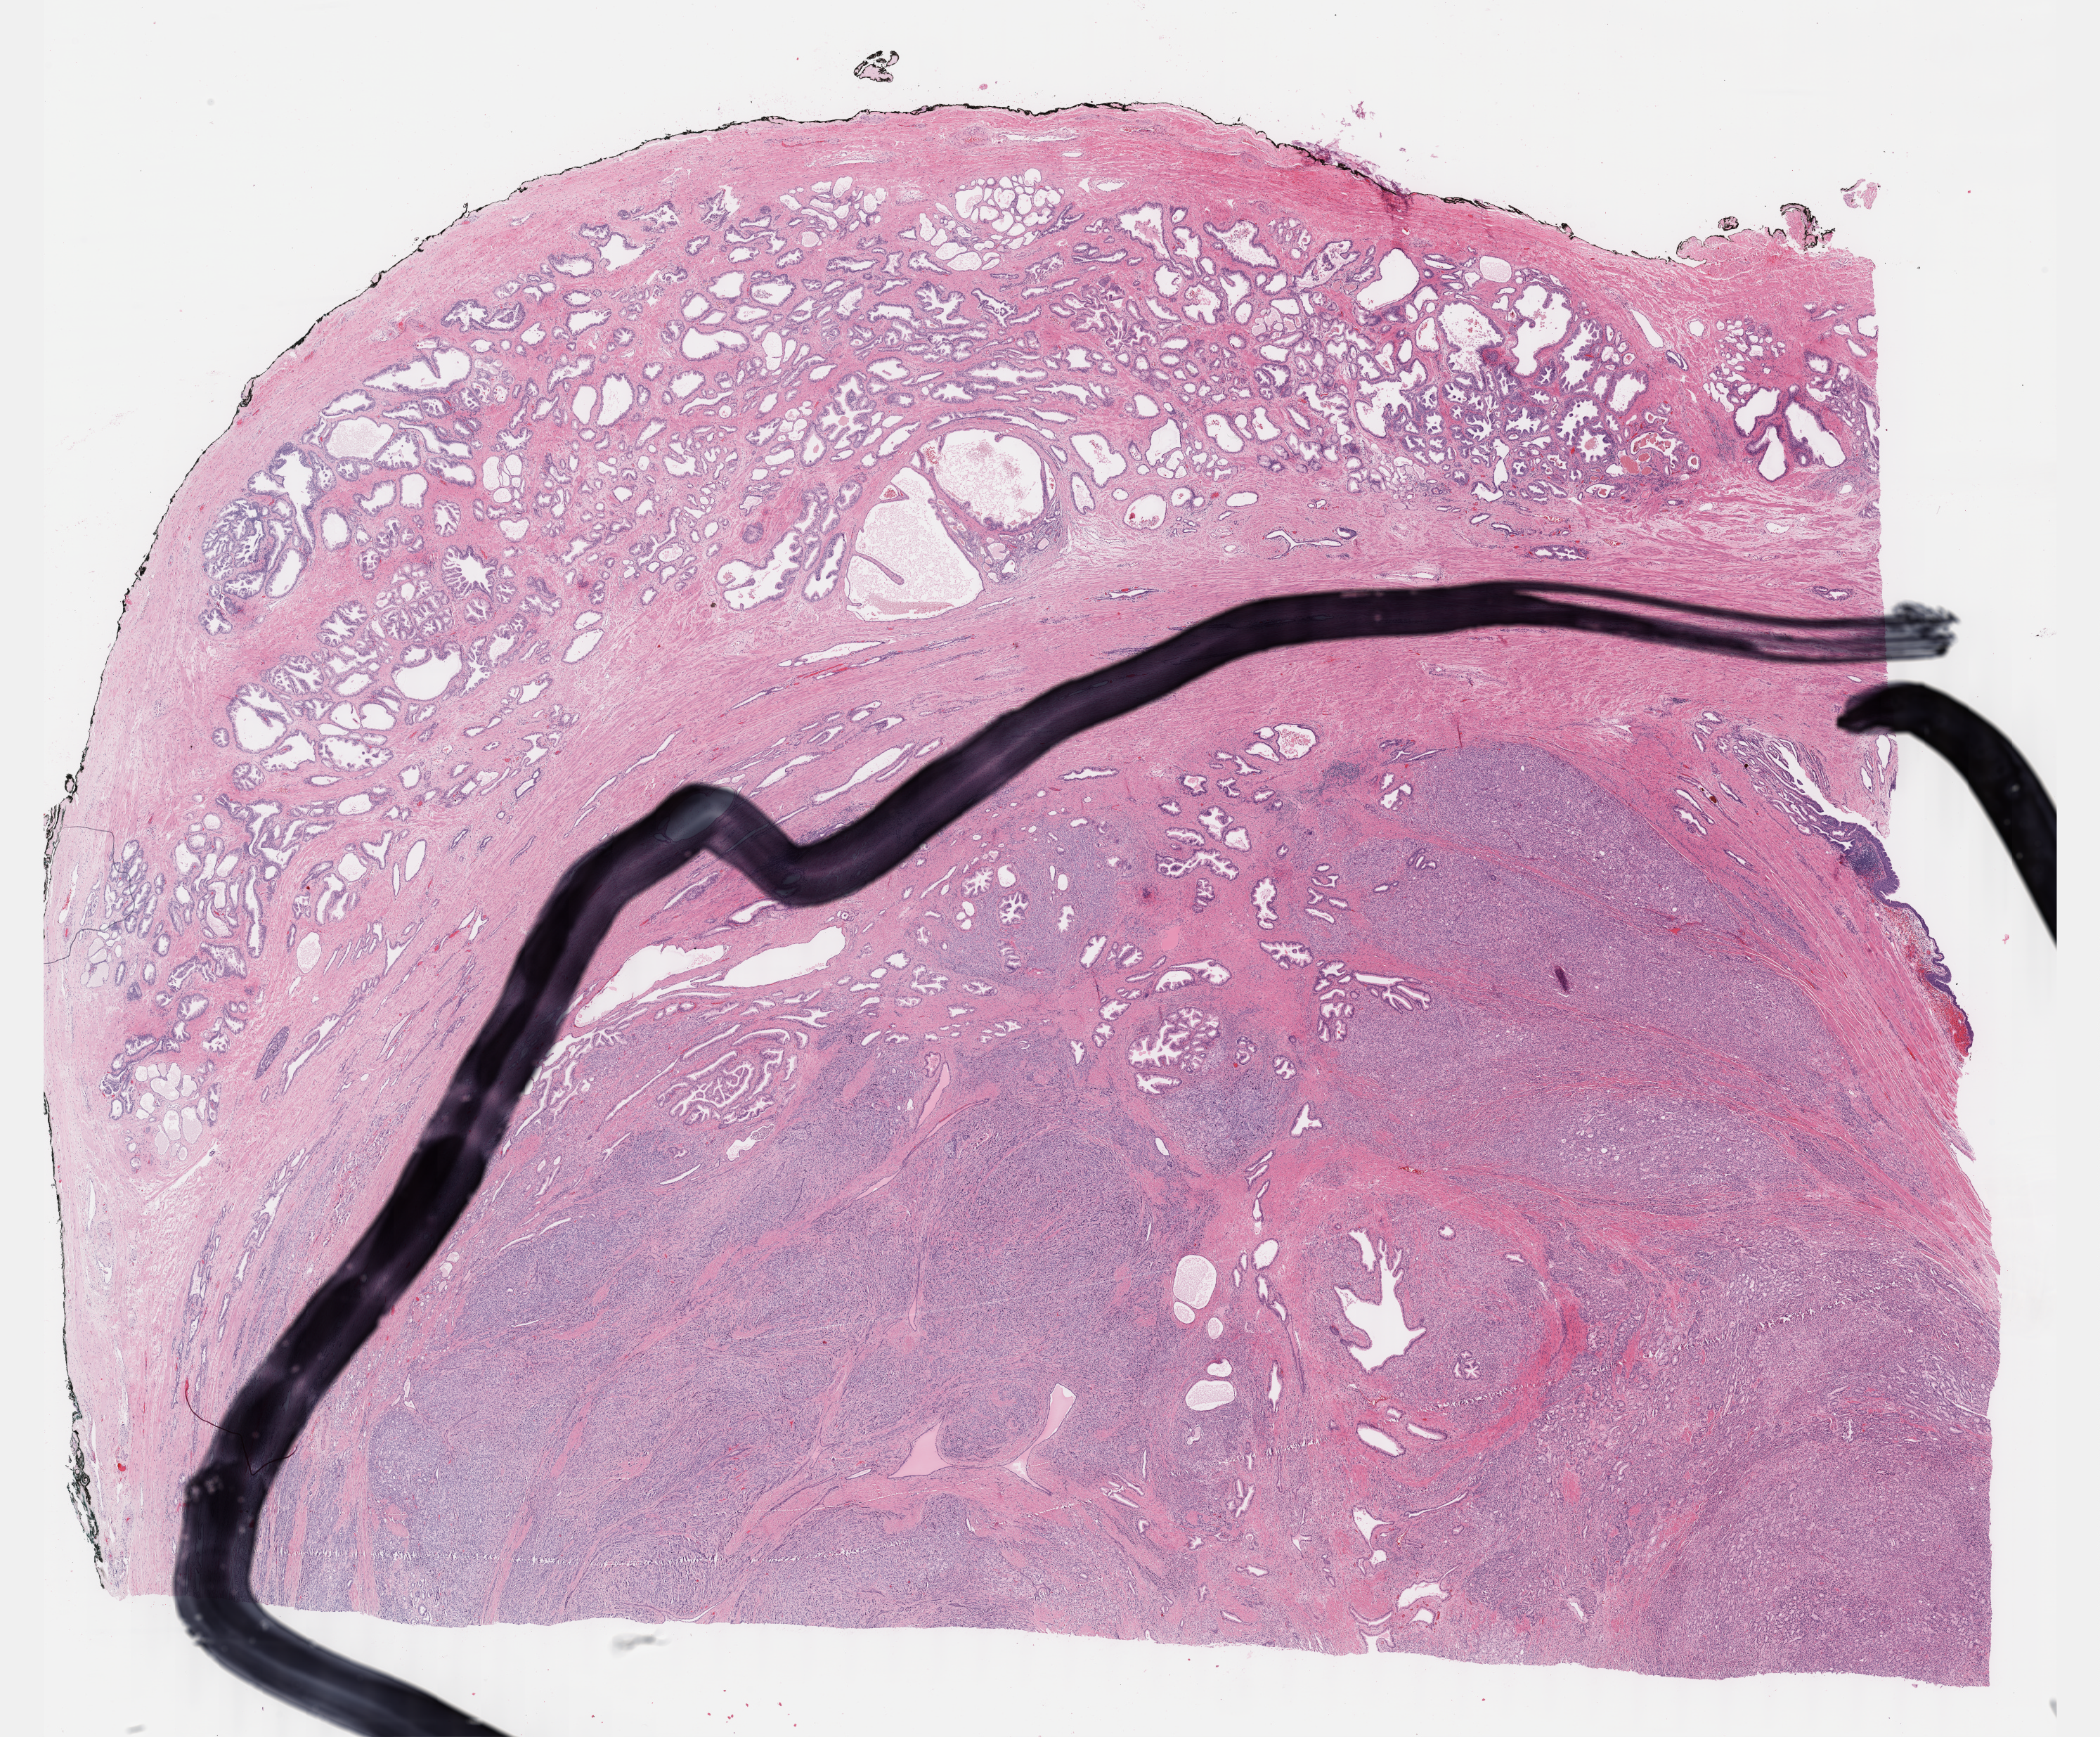
H&E-stained whole-slide image, a low-resolution overview of the entire scanned area, about 23.8 x 19.6 mm; formalin-fixed paraffin-embedded (FFPE) diagnostic section; sample: primary tumour, prostate. Patient: male, age at initial diagnosis 62 years. Gleason score: 9 (4+5).
Lymph nodes positive (case pathology): 0 of 3 examined. Pathologic diagnosis: Adenocarcinoma, NOS (prostate gland).